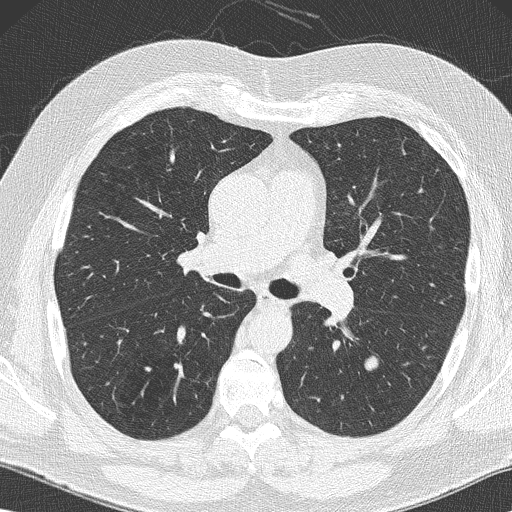
Chest CT (low-dose screening protocol), one axial image. Baseline screening round. Lung window (W 1500 / L -600 HU). 2 mm slice thickness. Lung (sharp) reconstruction kernel (B50f). Slice 67 of 152 in the series. 512 × 512 image matrix, field of view 350 × 350 mm. Male participant, aged 59 years at enrolment. Former smoker at enrolment.
Expert-annotated lung lesion, bounding box <348,348,391,383> (left, top, right, bottom; pixels). The screening reader recorded 2 non-calcified nodules or masses ≥4 mm on this exam (left lower lobe, left lower lobe); which of them this box marks is not recorded. Participant outcome: lung cancer diagnosed 61 days after this screen — large cell carcinoma, NOS, left lower lobe, poorly differentiated (G3), stage IA (AJCC 6th edition), 14 mm at pathology.